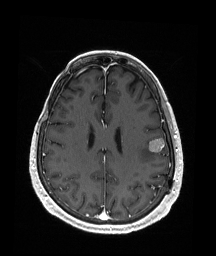
Brain MRI from a brain-tumour surgery series, one axial slice. Position 71 of 176 along the scan axis. T1-weighted post-contrast. 1 mm slice thickness. 216 × 256 image matrix, field of view 211 × 250 mm. Case-level facts recorded for this patient, not image findings: histopathology: Metastatic Malignant Melanoma.
Outlined on this slice (expert manual segmentation):
- tumour: bounding box <148,138,165,153> (left, top, right, bottom; pixels)